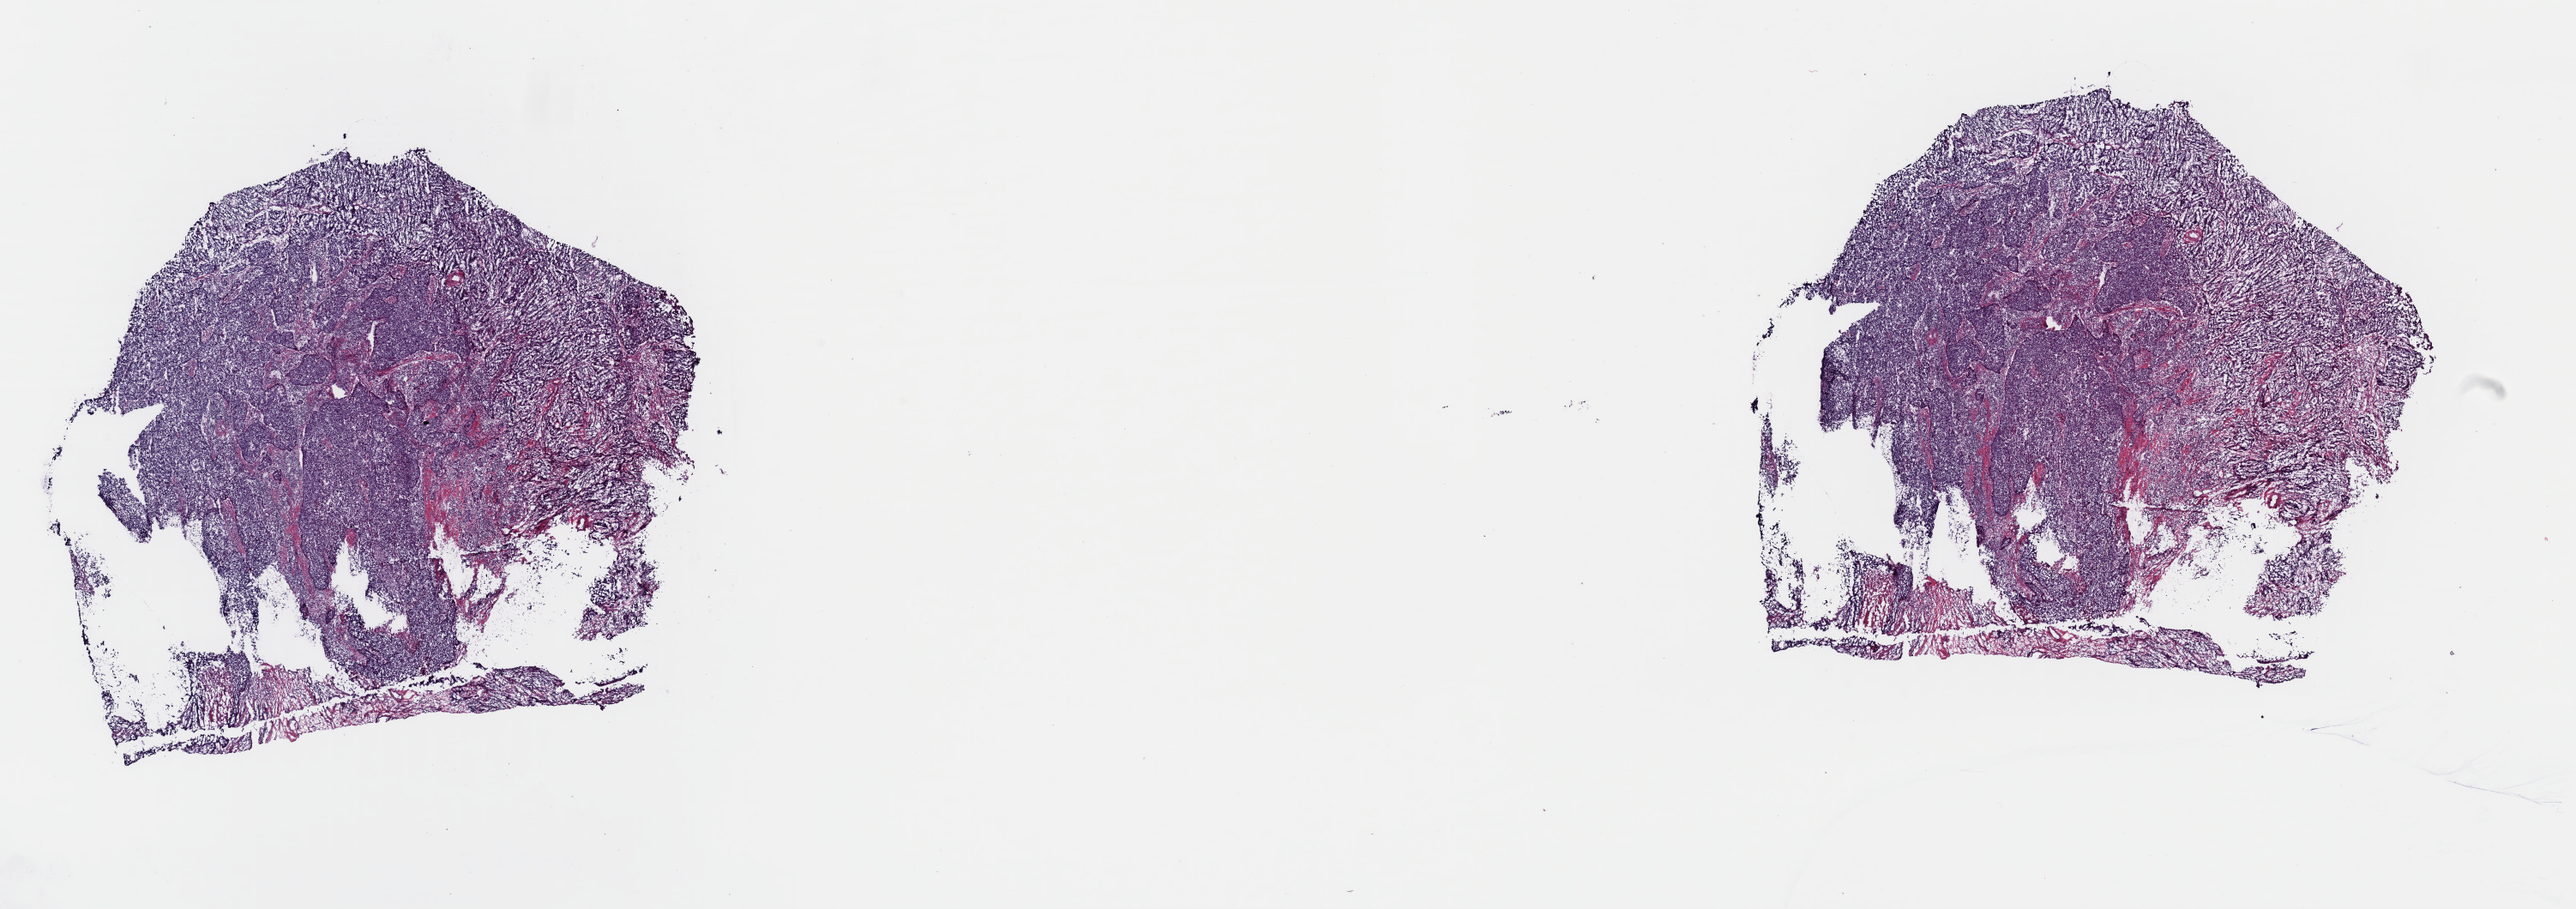
H&E-stained whole-slide image — low-resolution overview of the scanned area, about 23.7 x 8.4 mm (slide scanned at 40x), frozen section from the top of the tissue portion, cervix, primary tumour sample. Female patient; age at initial diagnosis 59 years. Histologic grade: G3 (poorly differentiated). Composition of this section per pathologist review: tumour cells 100%, tumour nuclei 80%, normal cells 0%, stromal cells 0%, necrosis 0%. Infiltration values recorded for this section: lymphocyte infiltration 13%, monocyte infiltration 0%, neutrophil infiltration 0%.
* FIGO stage: IIIB
* histologic diagnosis: Squamous cell carcinoma, NOS (cervix uteri)